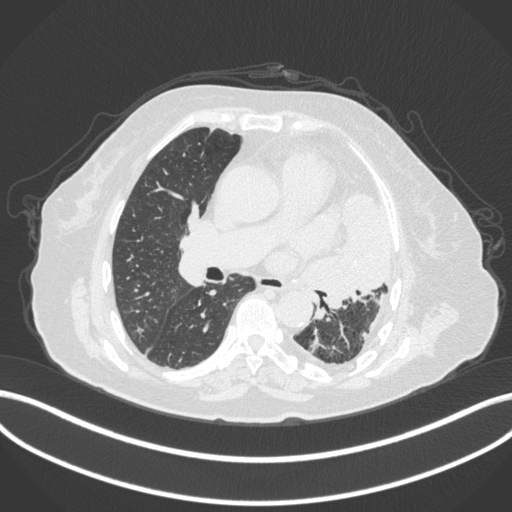
Chest CT, one axial slice. Position 200 of 399 along the scan axis. Reconstruction kernel B31f. 120 kVp. Lung window (W 1500 / L -600 HU). 1 mm slice thickness. 512 × 512 image matrix, field of view 400 × 400 mm. Patient: female, 75 years. From the clinical record (not read from this slice): clinical TNM (as recorded): T3 N3 M1.
Outlined on this slice (bounding box drawn by a radiologist):
- lung tumour (recorded histology: adenocarcinoma): bounding box (x1, y1, x2, y2) in pixels: (310, 190, 398, 312)